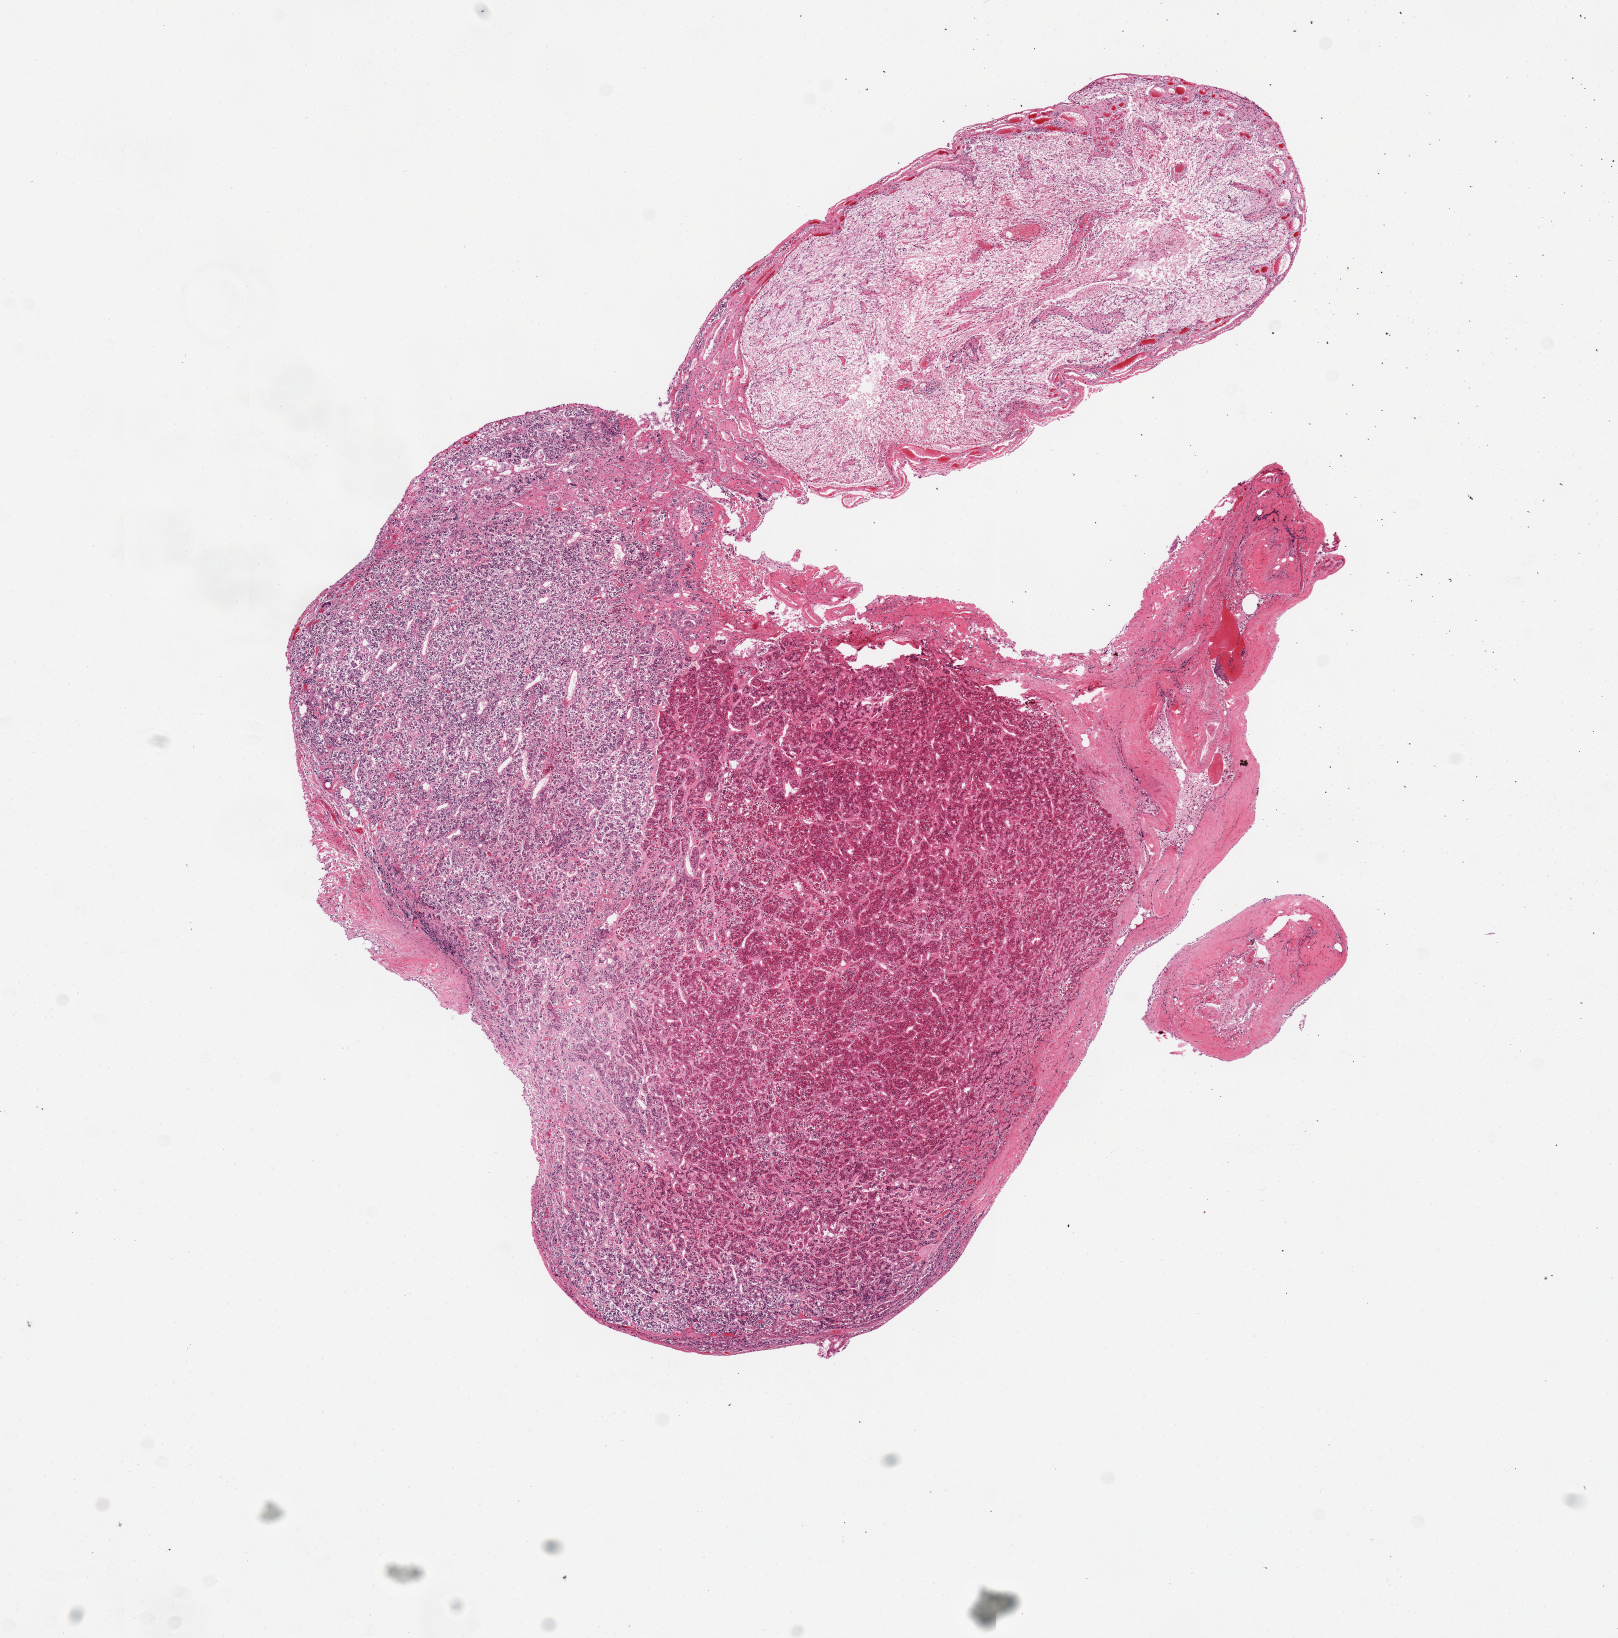
Whole-slide image, haematoxylin and eosin stain — low-resolution overview of the scanned area, about 12.8 x 13.0 mm; PAXgene-fixed paraffin-embedded (PFPE) section; section of pituitary (target tissue); tissue donor sample.
Pathologist's review note for this sample: 1 piece; anterior and posterior.